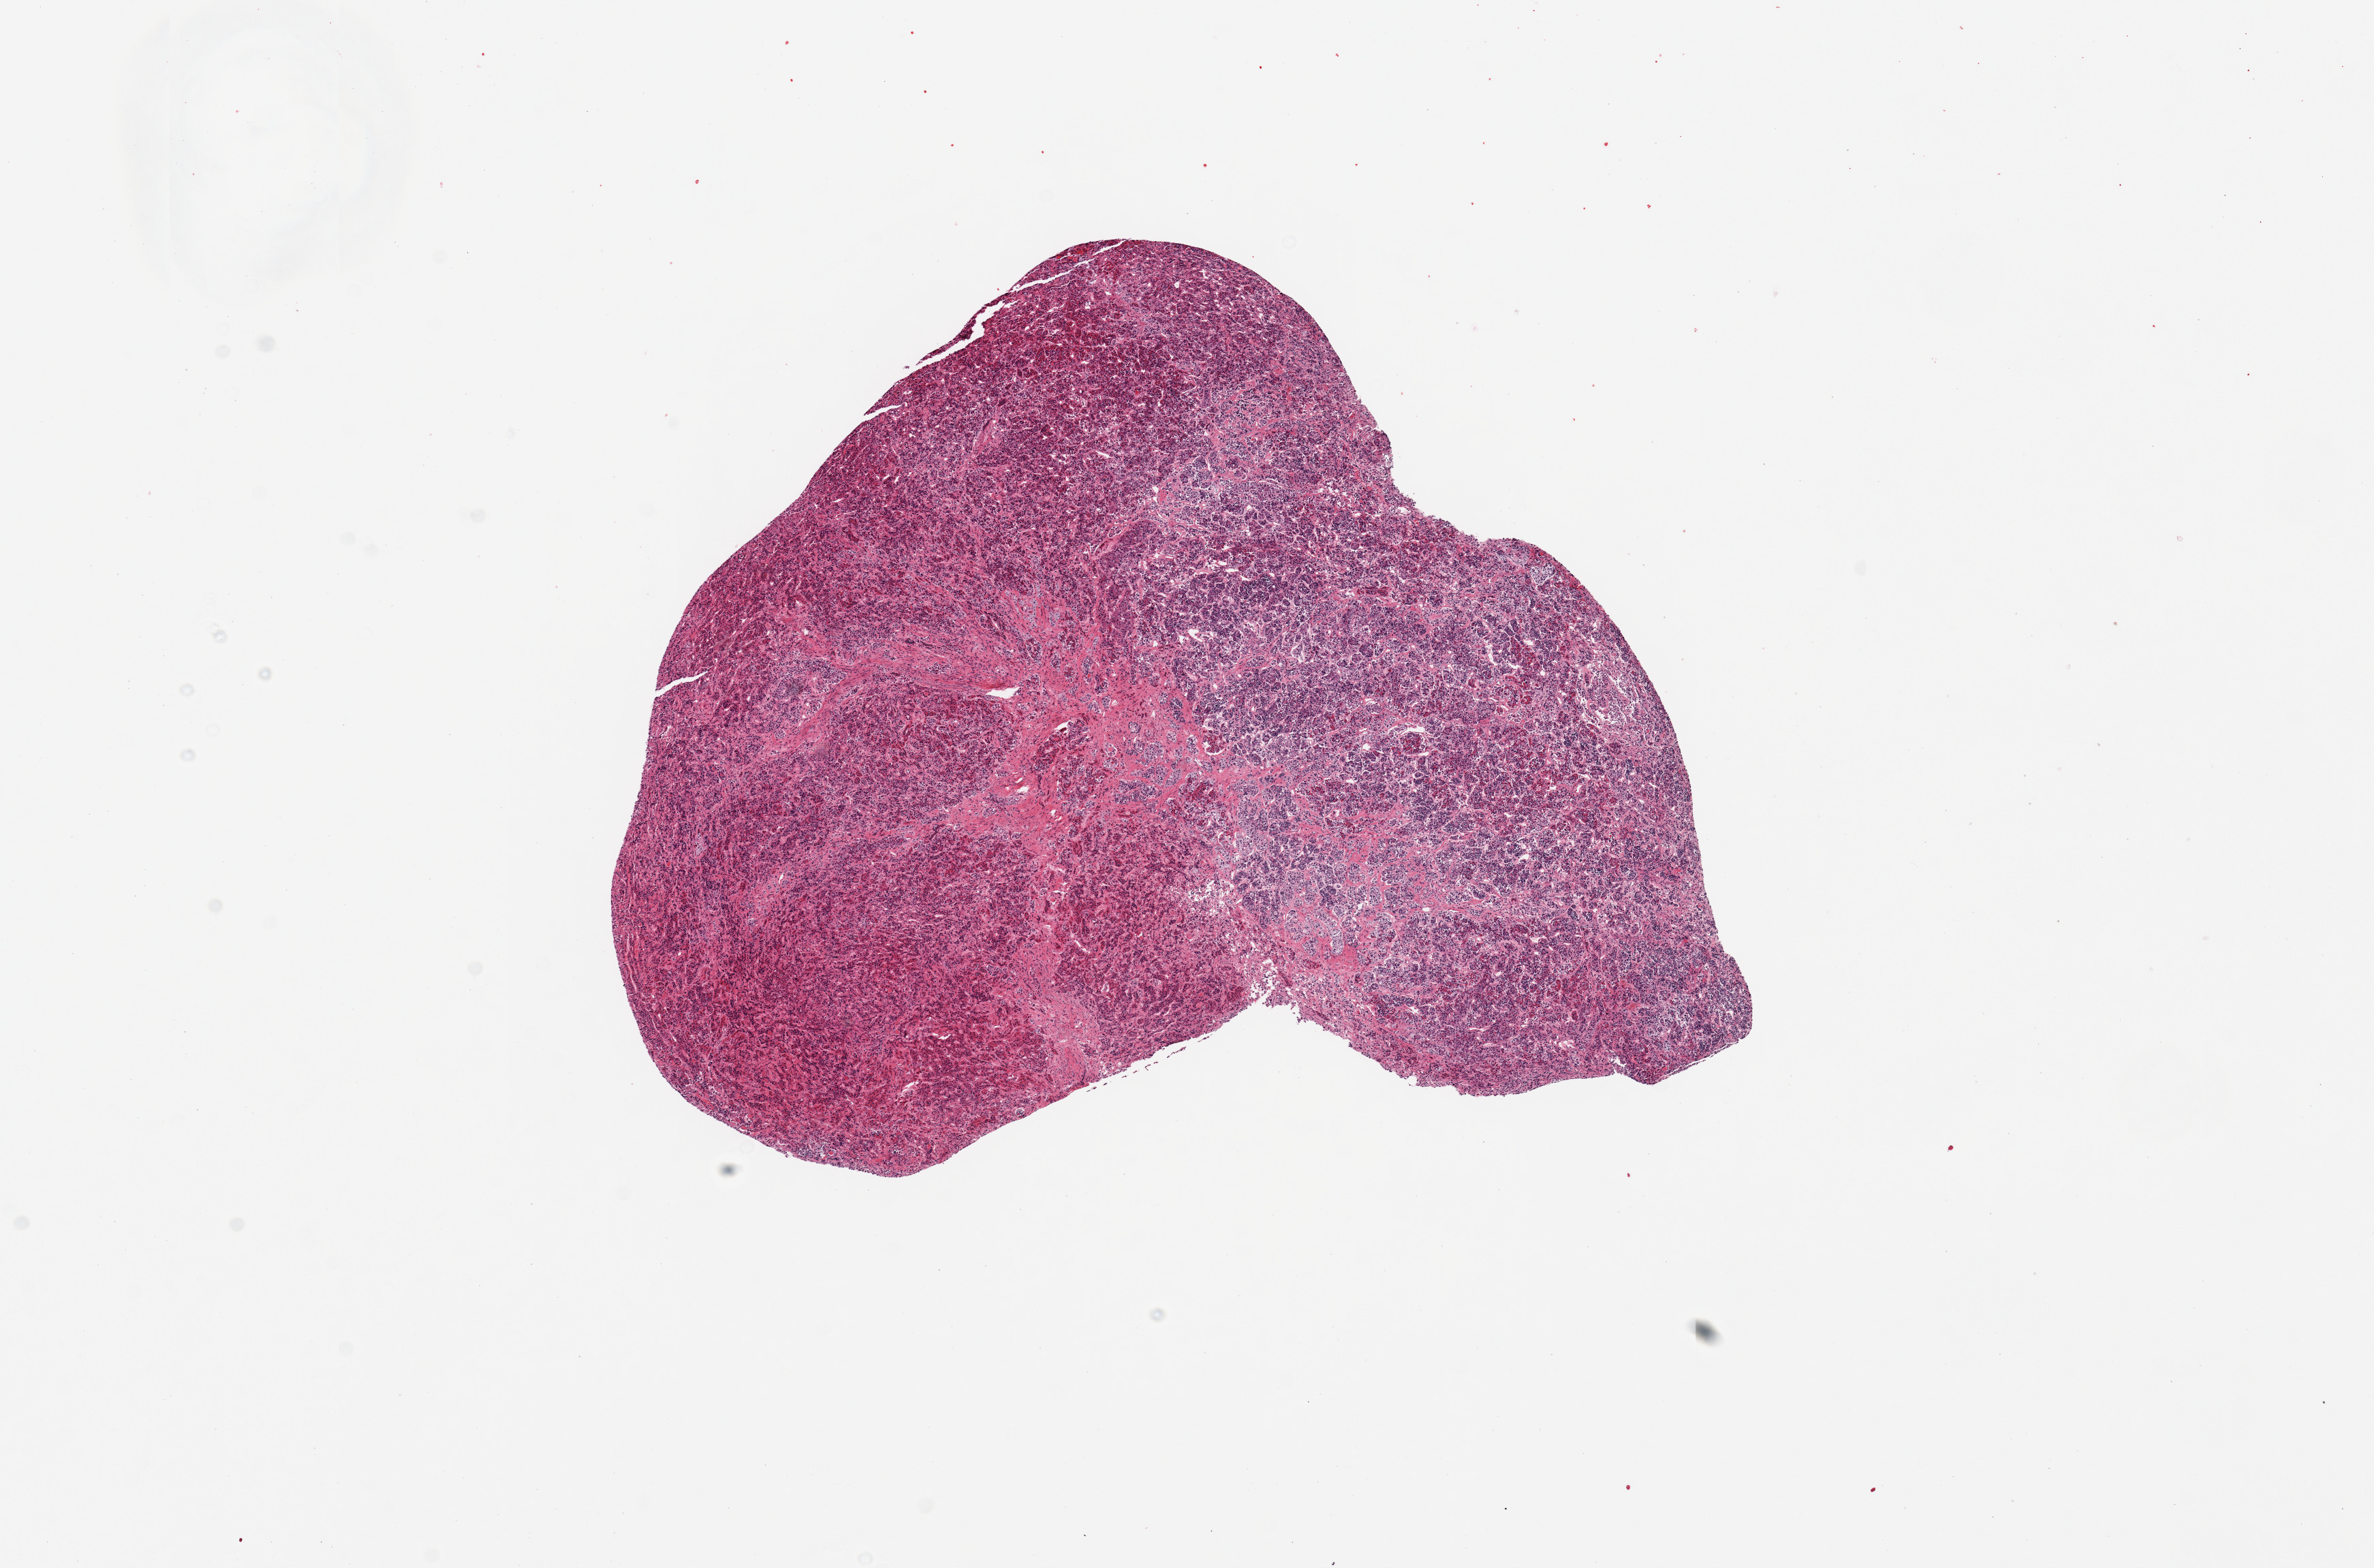
Digitized H&E-stained section, brightfield, shown as a low-resolution overview of the whole scanned area (about 13.8 x 9.1 mm); PAXgene-fixed paraffin-embedded (PFPE) section; target tissue: pituitary; donor tissue sample. Male donor.
Pathologist's review note for this sample: 1 piece; only anterior portion.